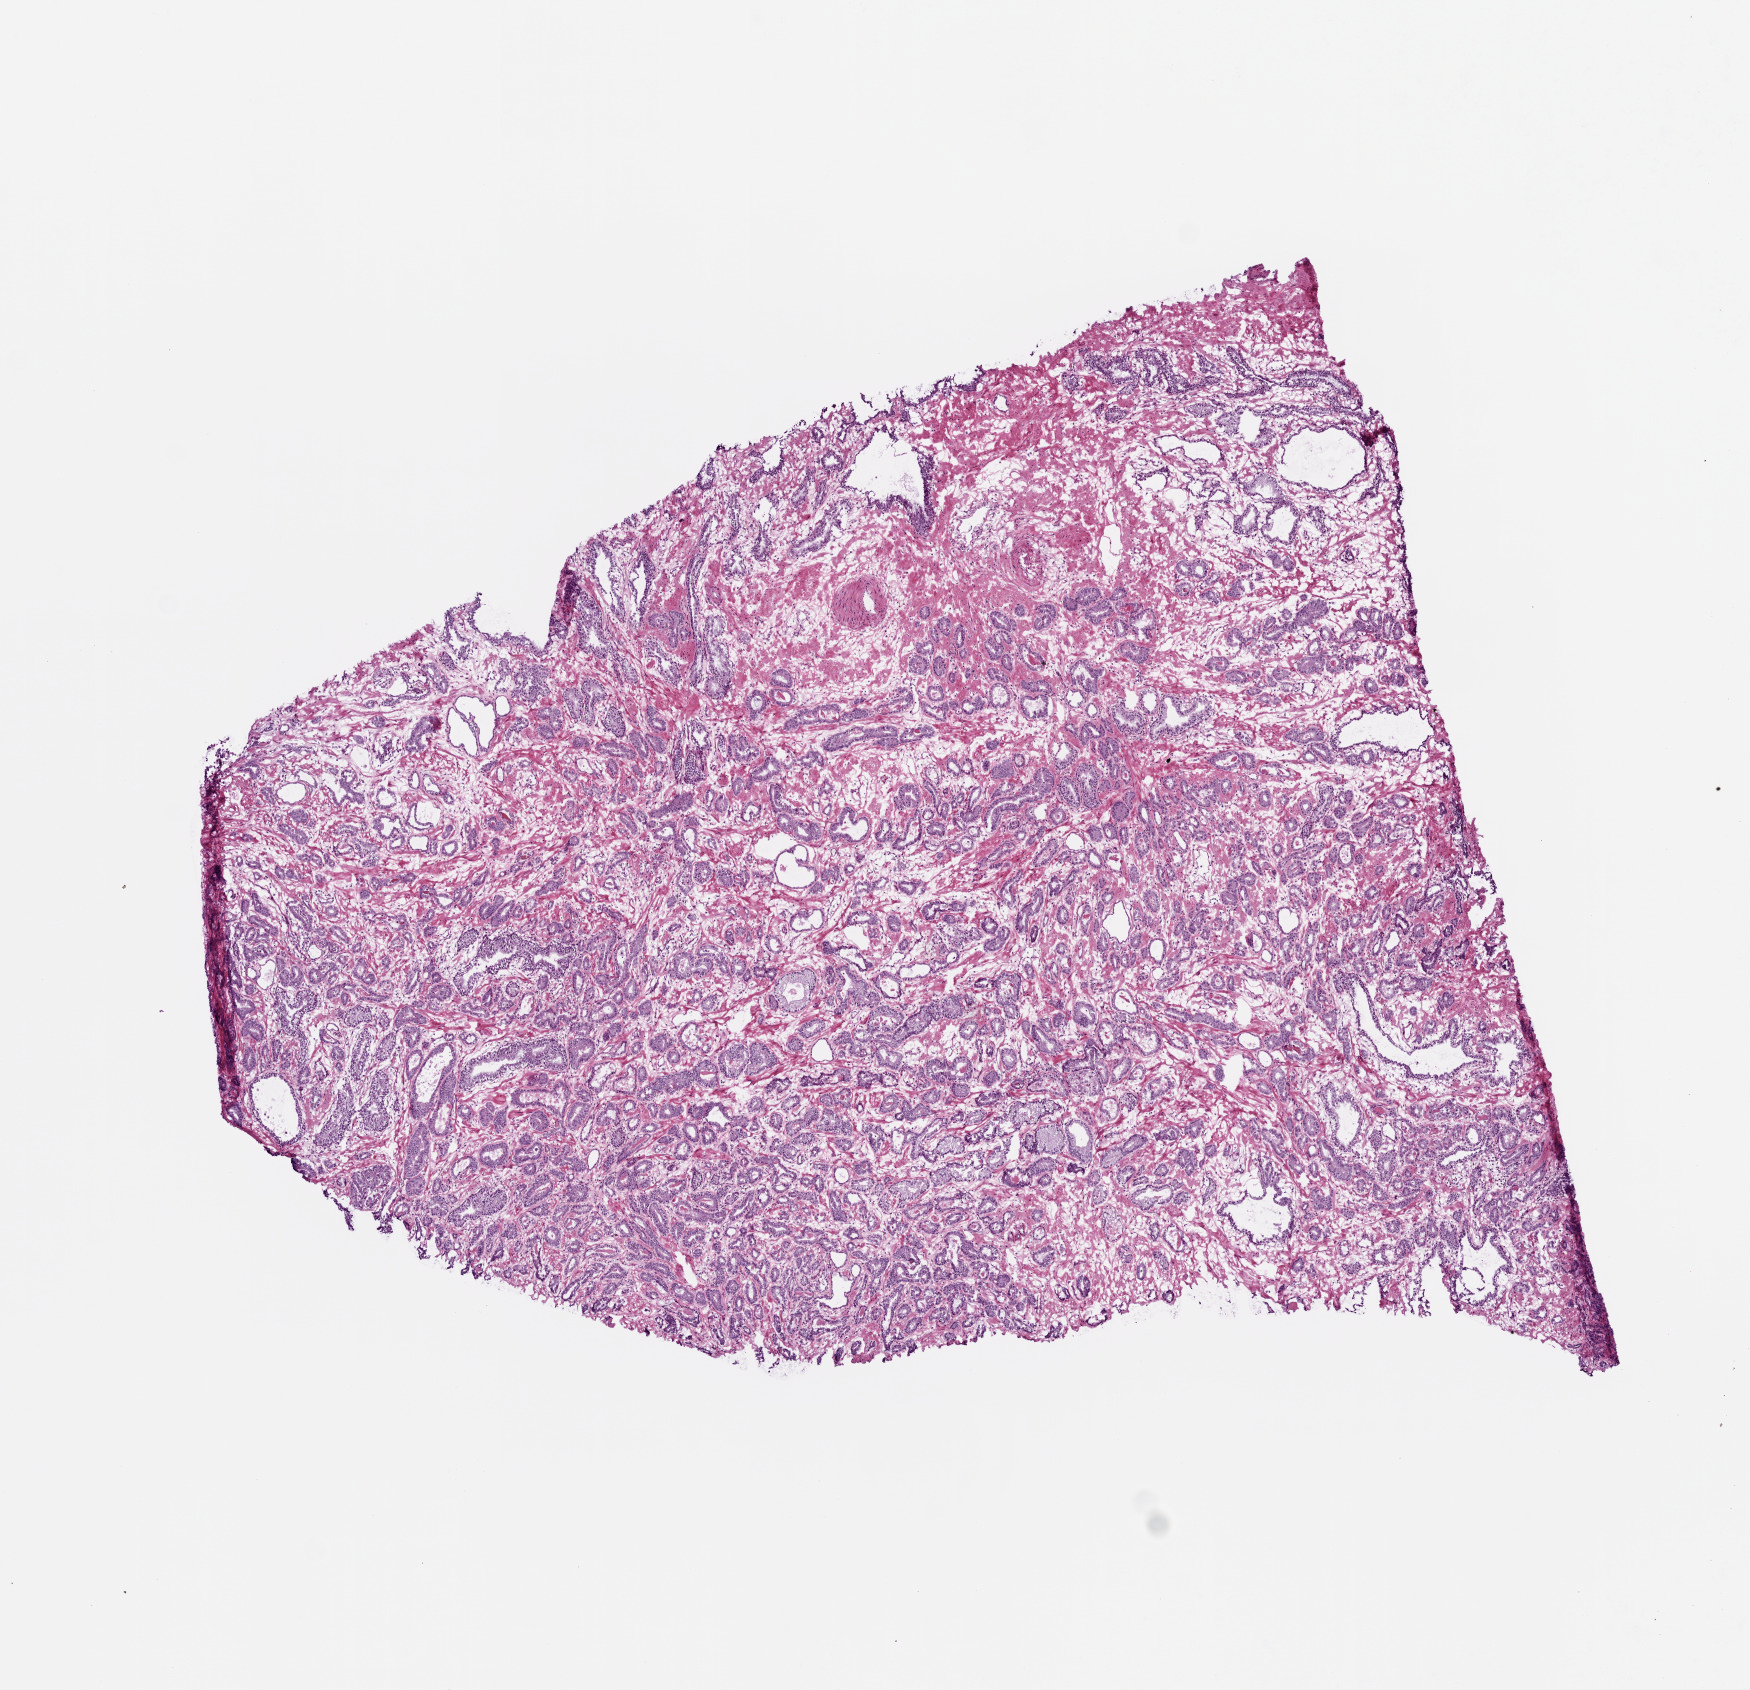
Digitized Hematoxylin and eosin (H&E) stained tissue section (whole slide), low-resolution overview of the scanned area, about 7.0 x 6.8 mm (slide scanned at 20x); frozen section from the top of the tissue portion; prostate, primary tumour sample. Male, age 57 years at initial diagnosis. Gleason score: 7 (3+4). Pathologist review of this section (percent, as recorded): tumour cells 60%, tumour nuclei 70%, normal cells 15%, stromal cells 25%, necrosis 0%. Inflammatory infiltration, as recorded: lymphocyte infiltration 0%, monocyte infiltration 0%, neutrophil infiltration 0%.
Laterality: bilateral. Lymph nodes positive (case pathology): 0 of 2 examined. Histologic diagnosis: Acinar cell carcinoma (prostate gland).